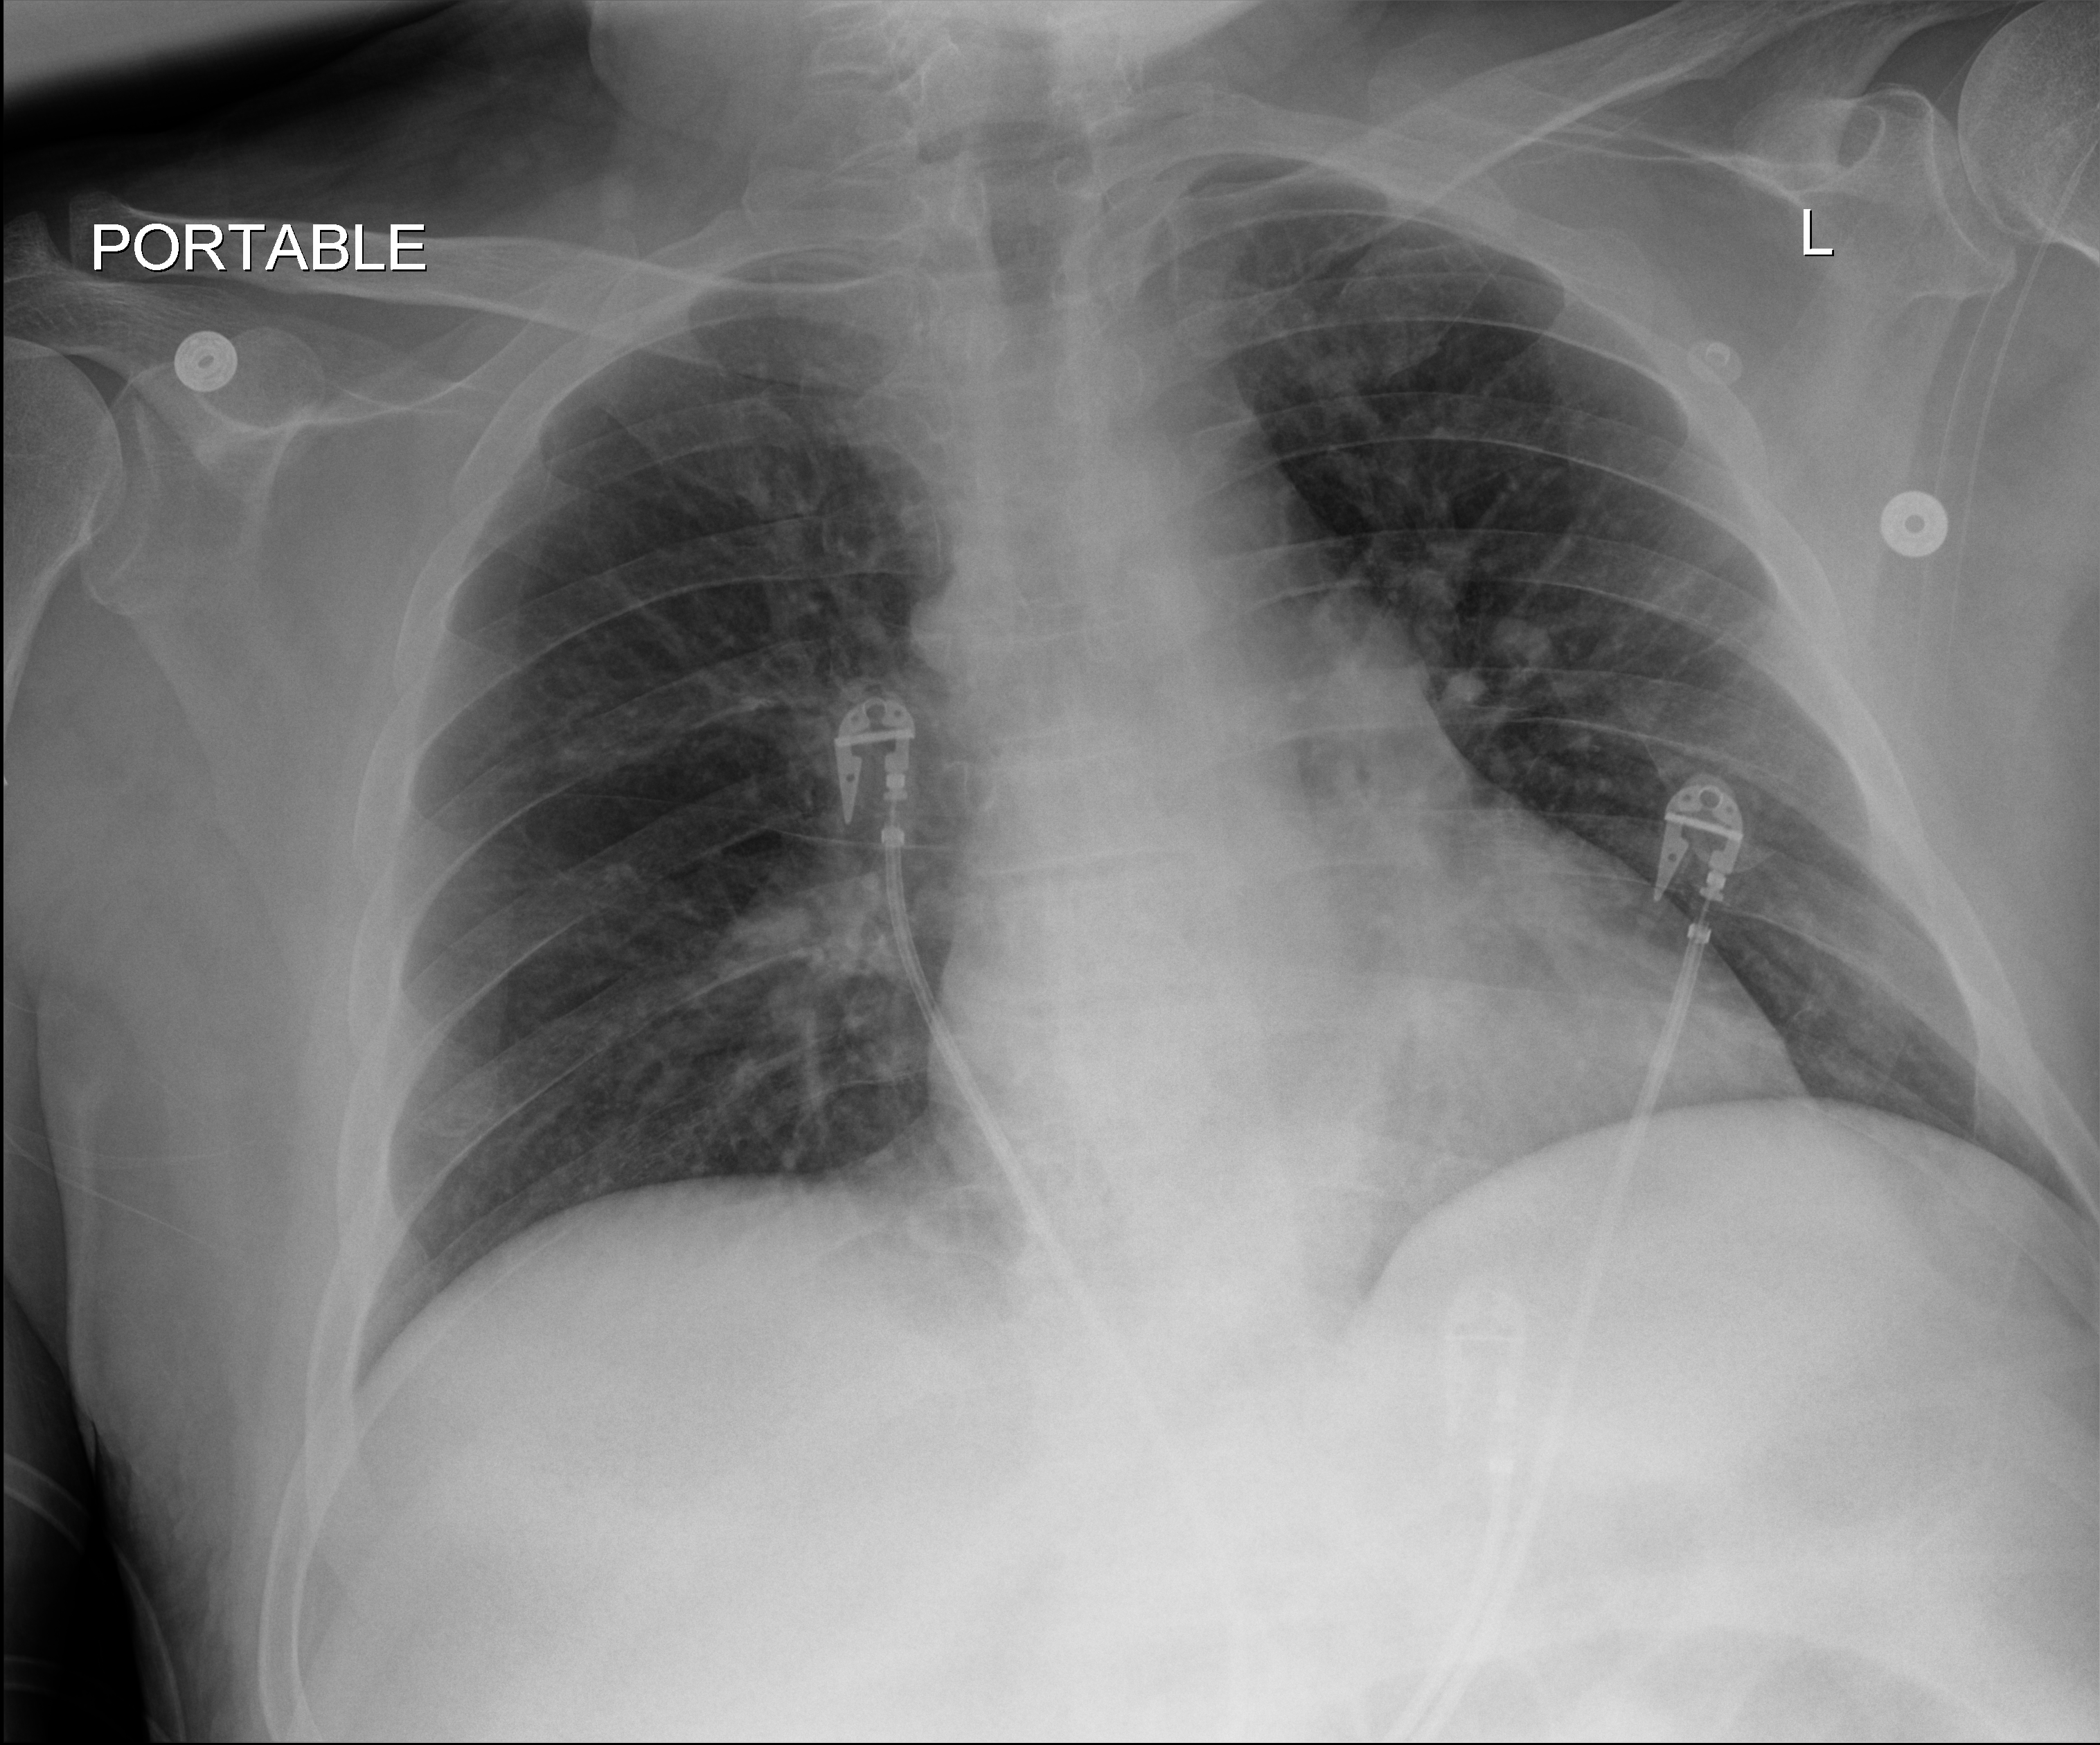
Bedside chest radiograph (digital radiography); anteroposterior (AP) projection. Patient hospitalised with COVID-19; male, aged 18–59 years.
From the hospital-stay record, not from the radiograph (when in the stay this image was taken is not recorded): admitted to intensive care during this hospital stay: yes; mechanically ventilated during this hospital stay: no; length of hospital stay: 15 days.